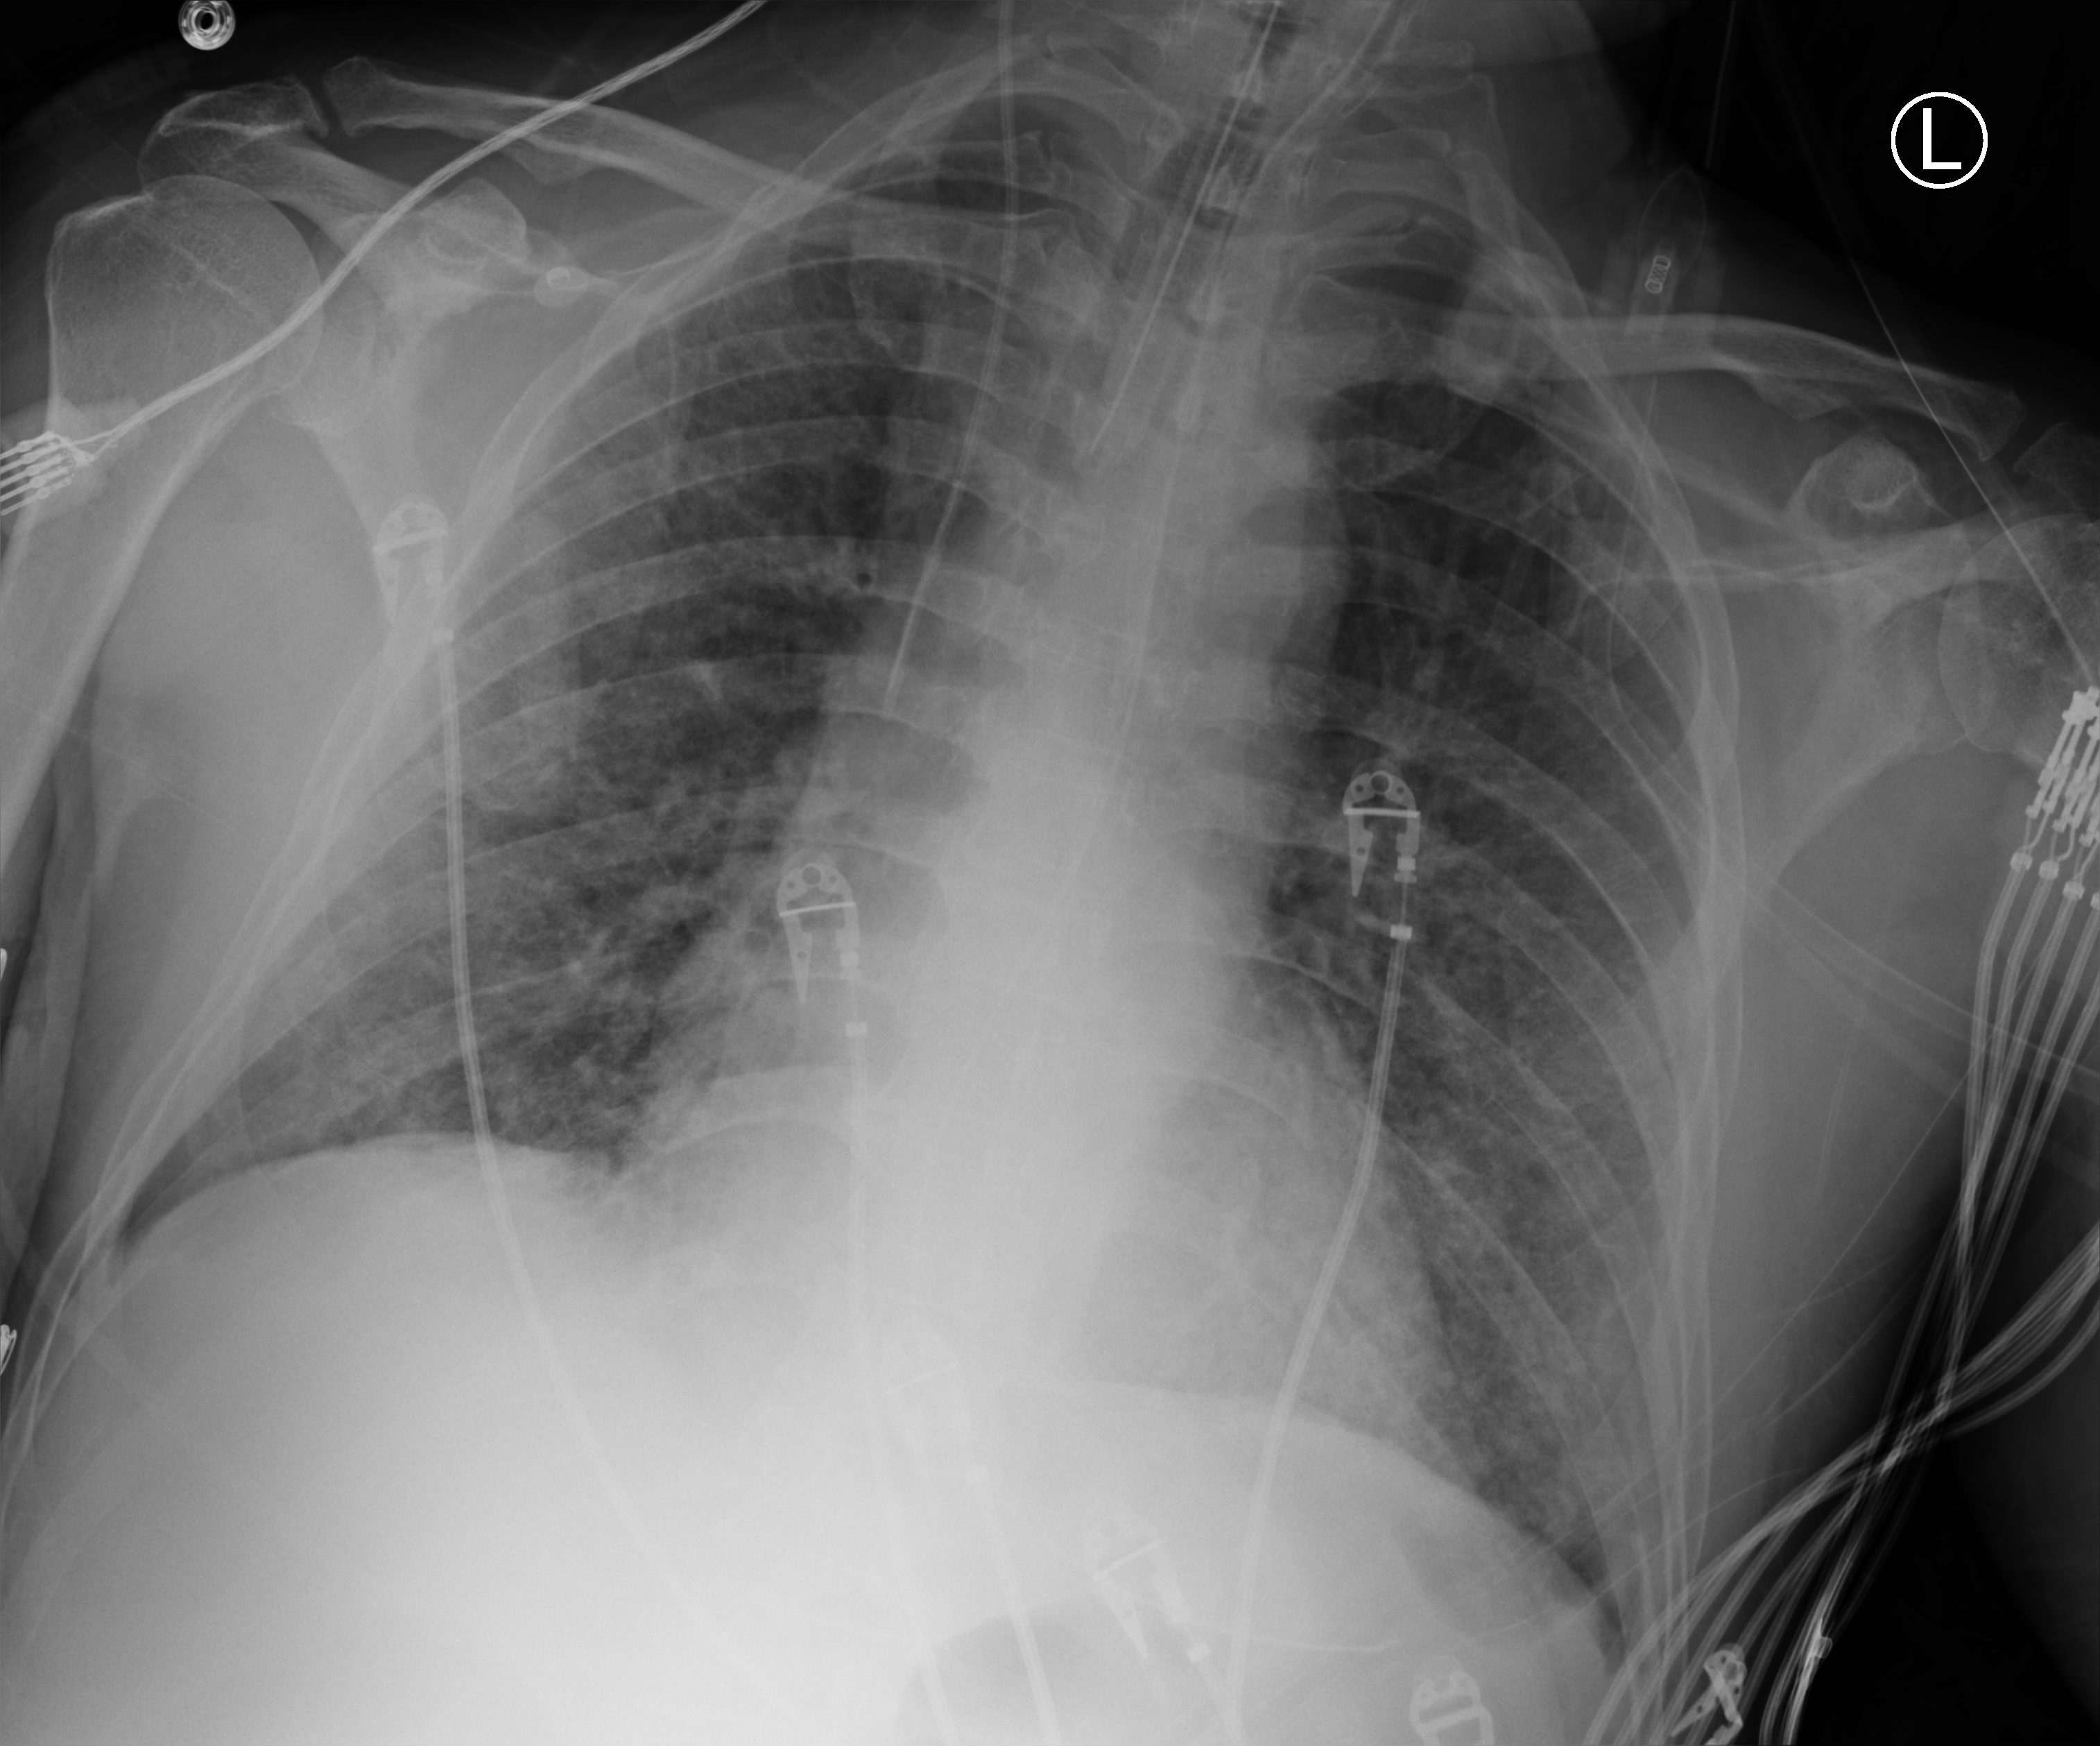
Chest X-ray (portable), anteroposterior (AP) projection. Patient hospitalised with COVID-19; male, aged 60–74 years.
Admission-level facts for this patient (not findings on this image; timing relative to this image not recorded):
- chronic kidney disease (admission record): no
- smoking status (admission record): never
- mechanically ventilated during this hospital stay: yes